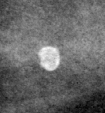
Region of interest cut from a scanned film mammogram (one marked finding), right breast, MLO view.
- Calcifications, morphology round and regular / lucent centered; BI-RADS assessment category 2; benign; no additional work-up was recommended (benign without callback).